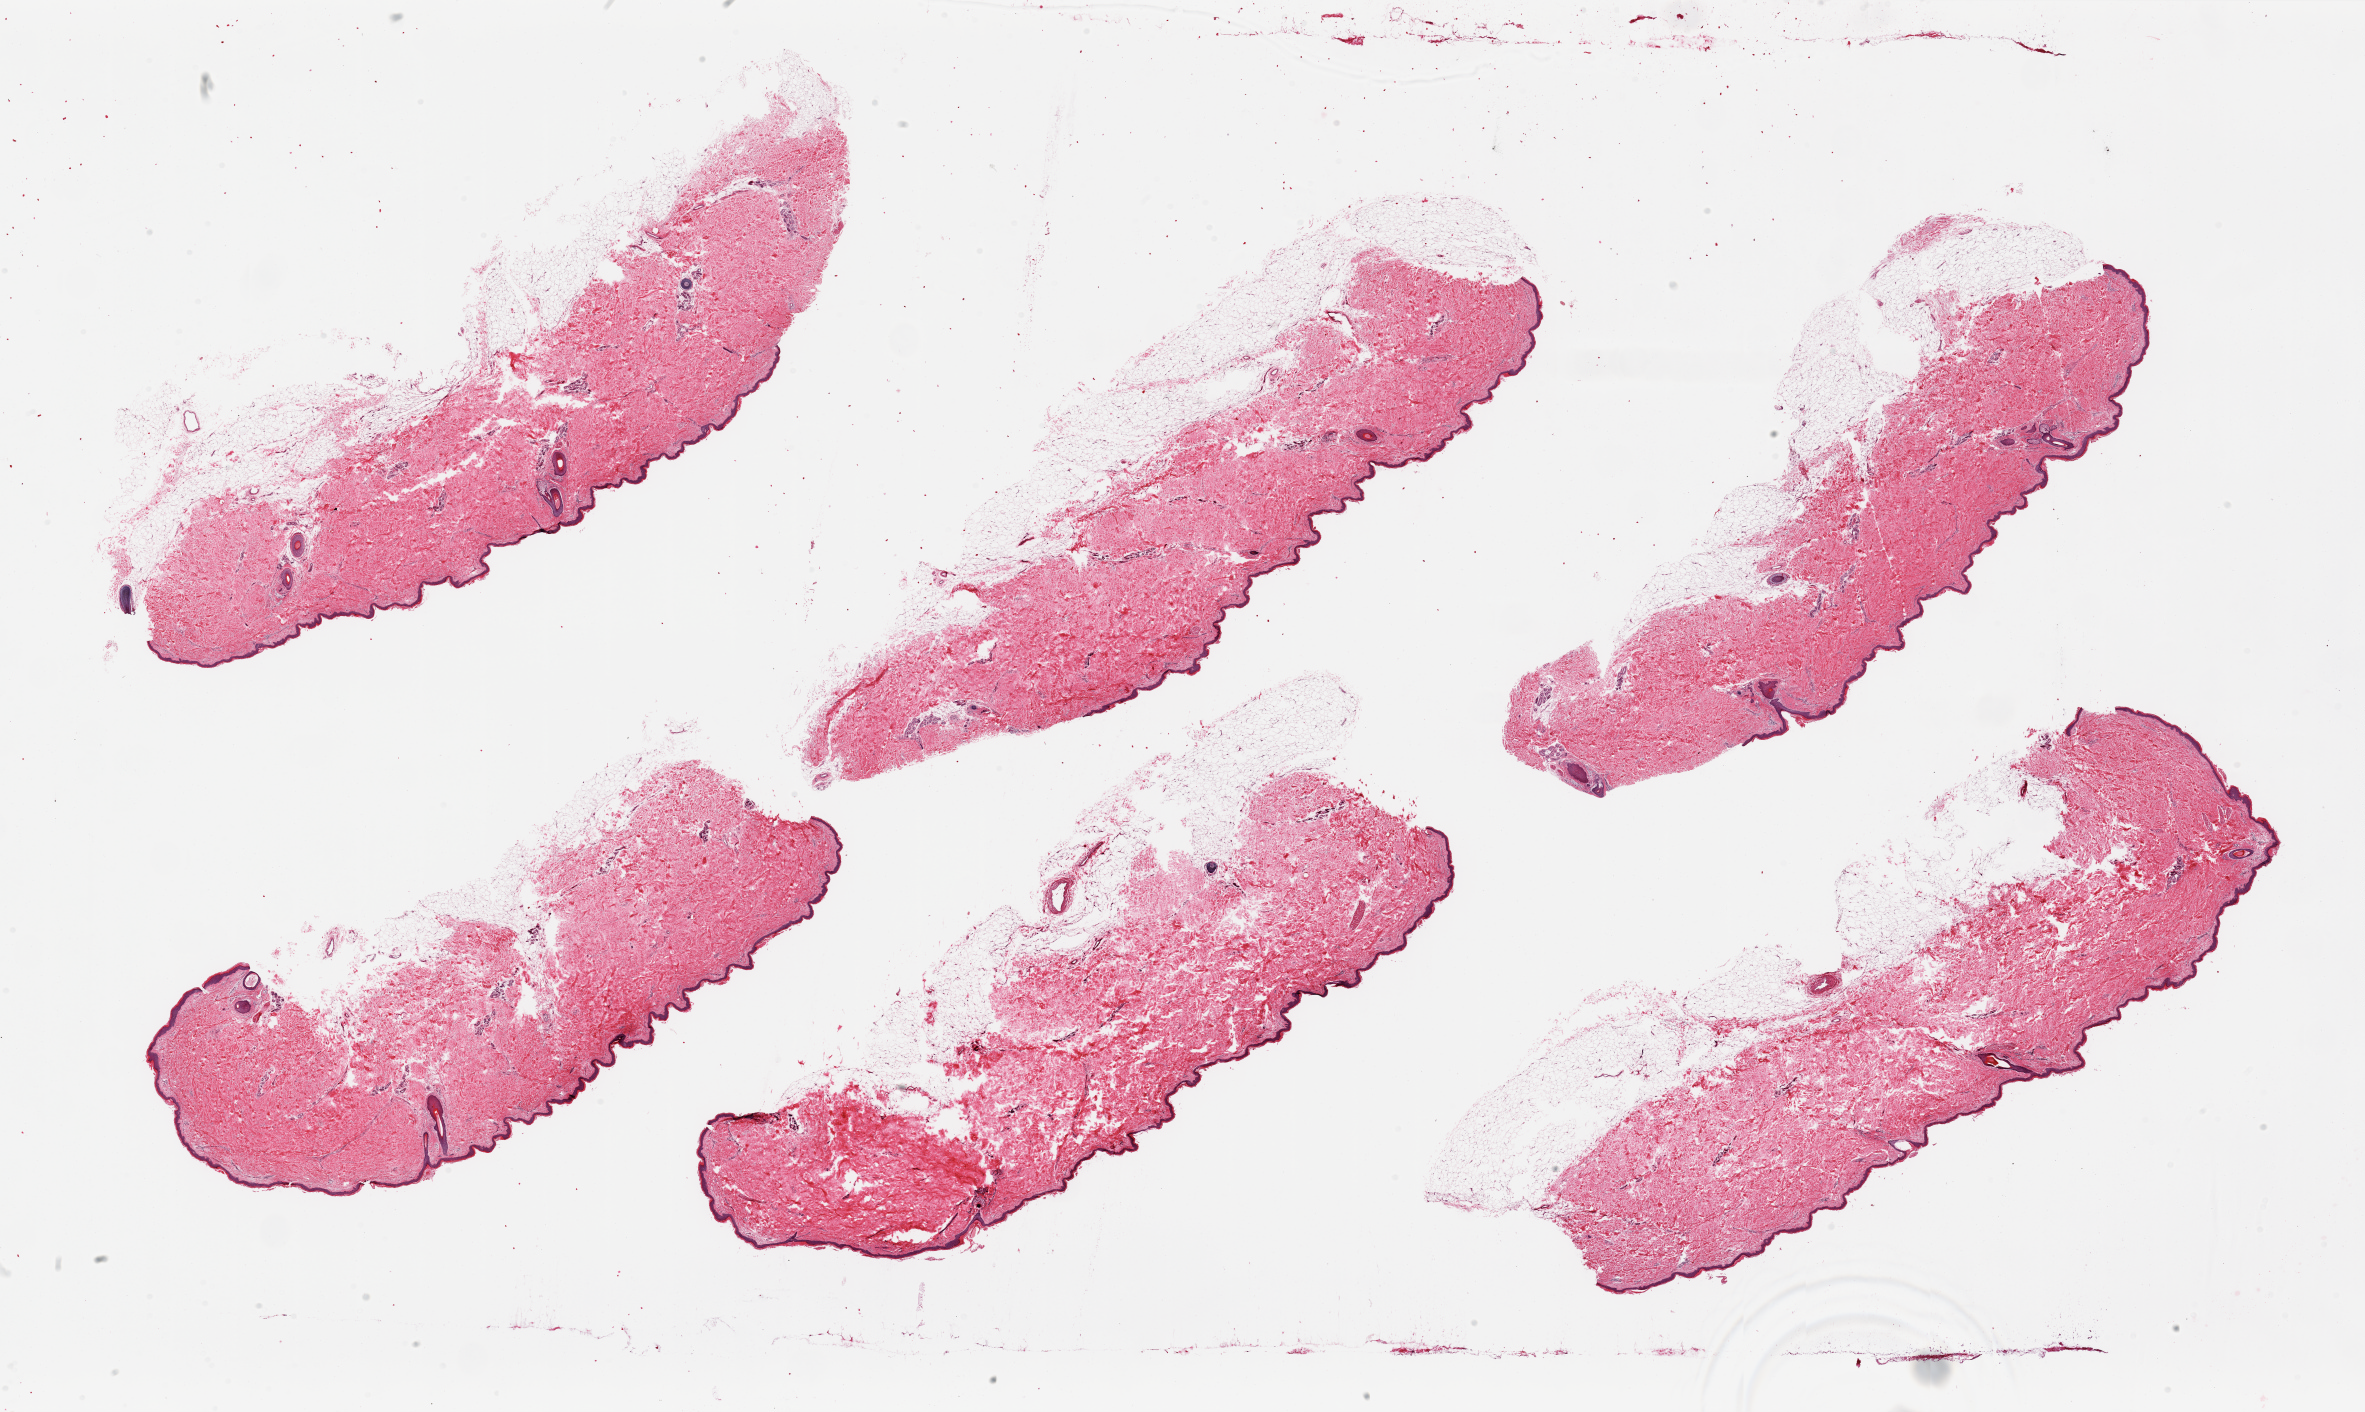
Digitized hematoxylin and eosin (H&E)-stained section, brightfield, a low-resolution overview of the entire scanned area, about 37.4 x 22.3 mm. PAXgene-fixed paraffin-embedded (PFPE) section. Sampled site (target tissue): skin of lower leg. Donor tissue sample. Male donor.
Review note (as recorded): 6 pieces; includes up to 30% attached fat, epidermis measures 33 microns.